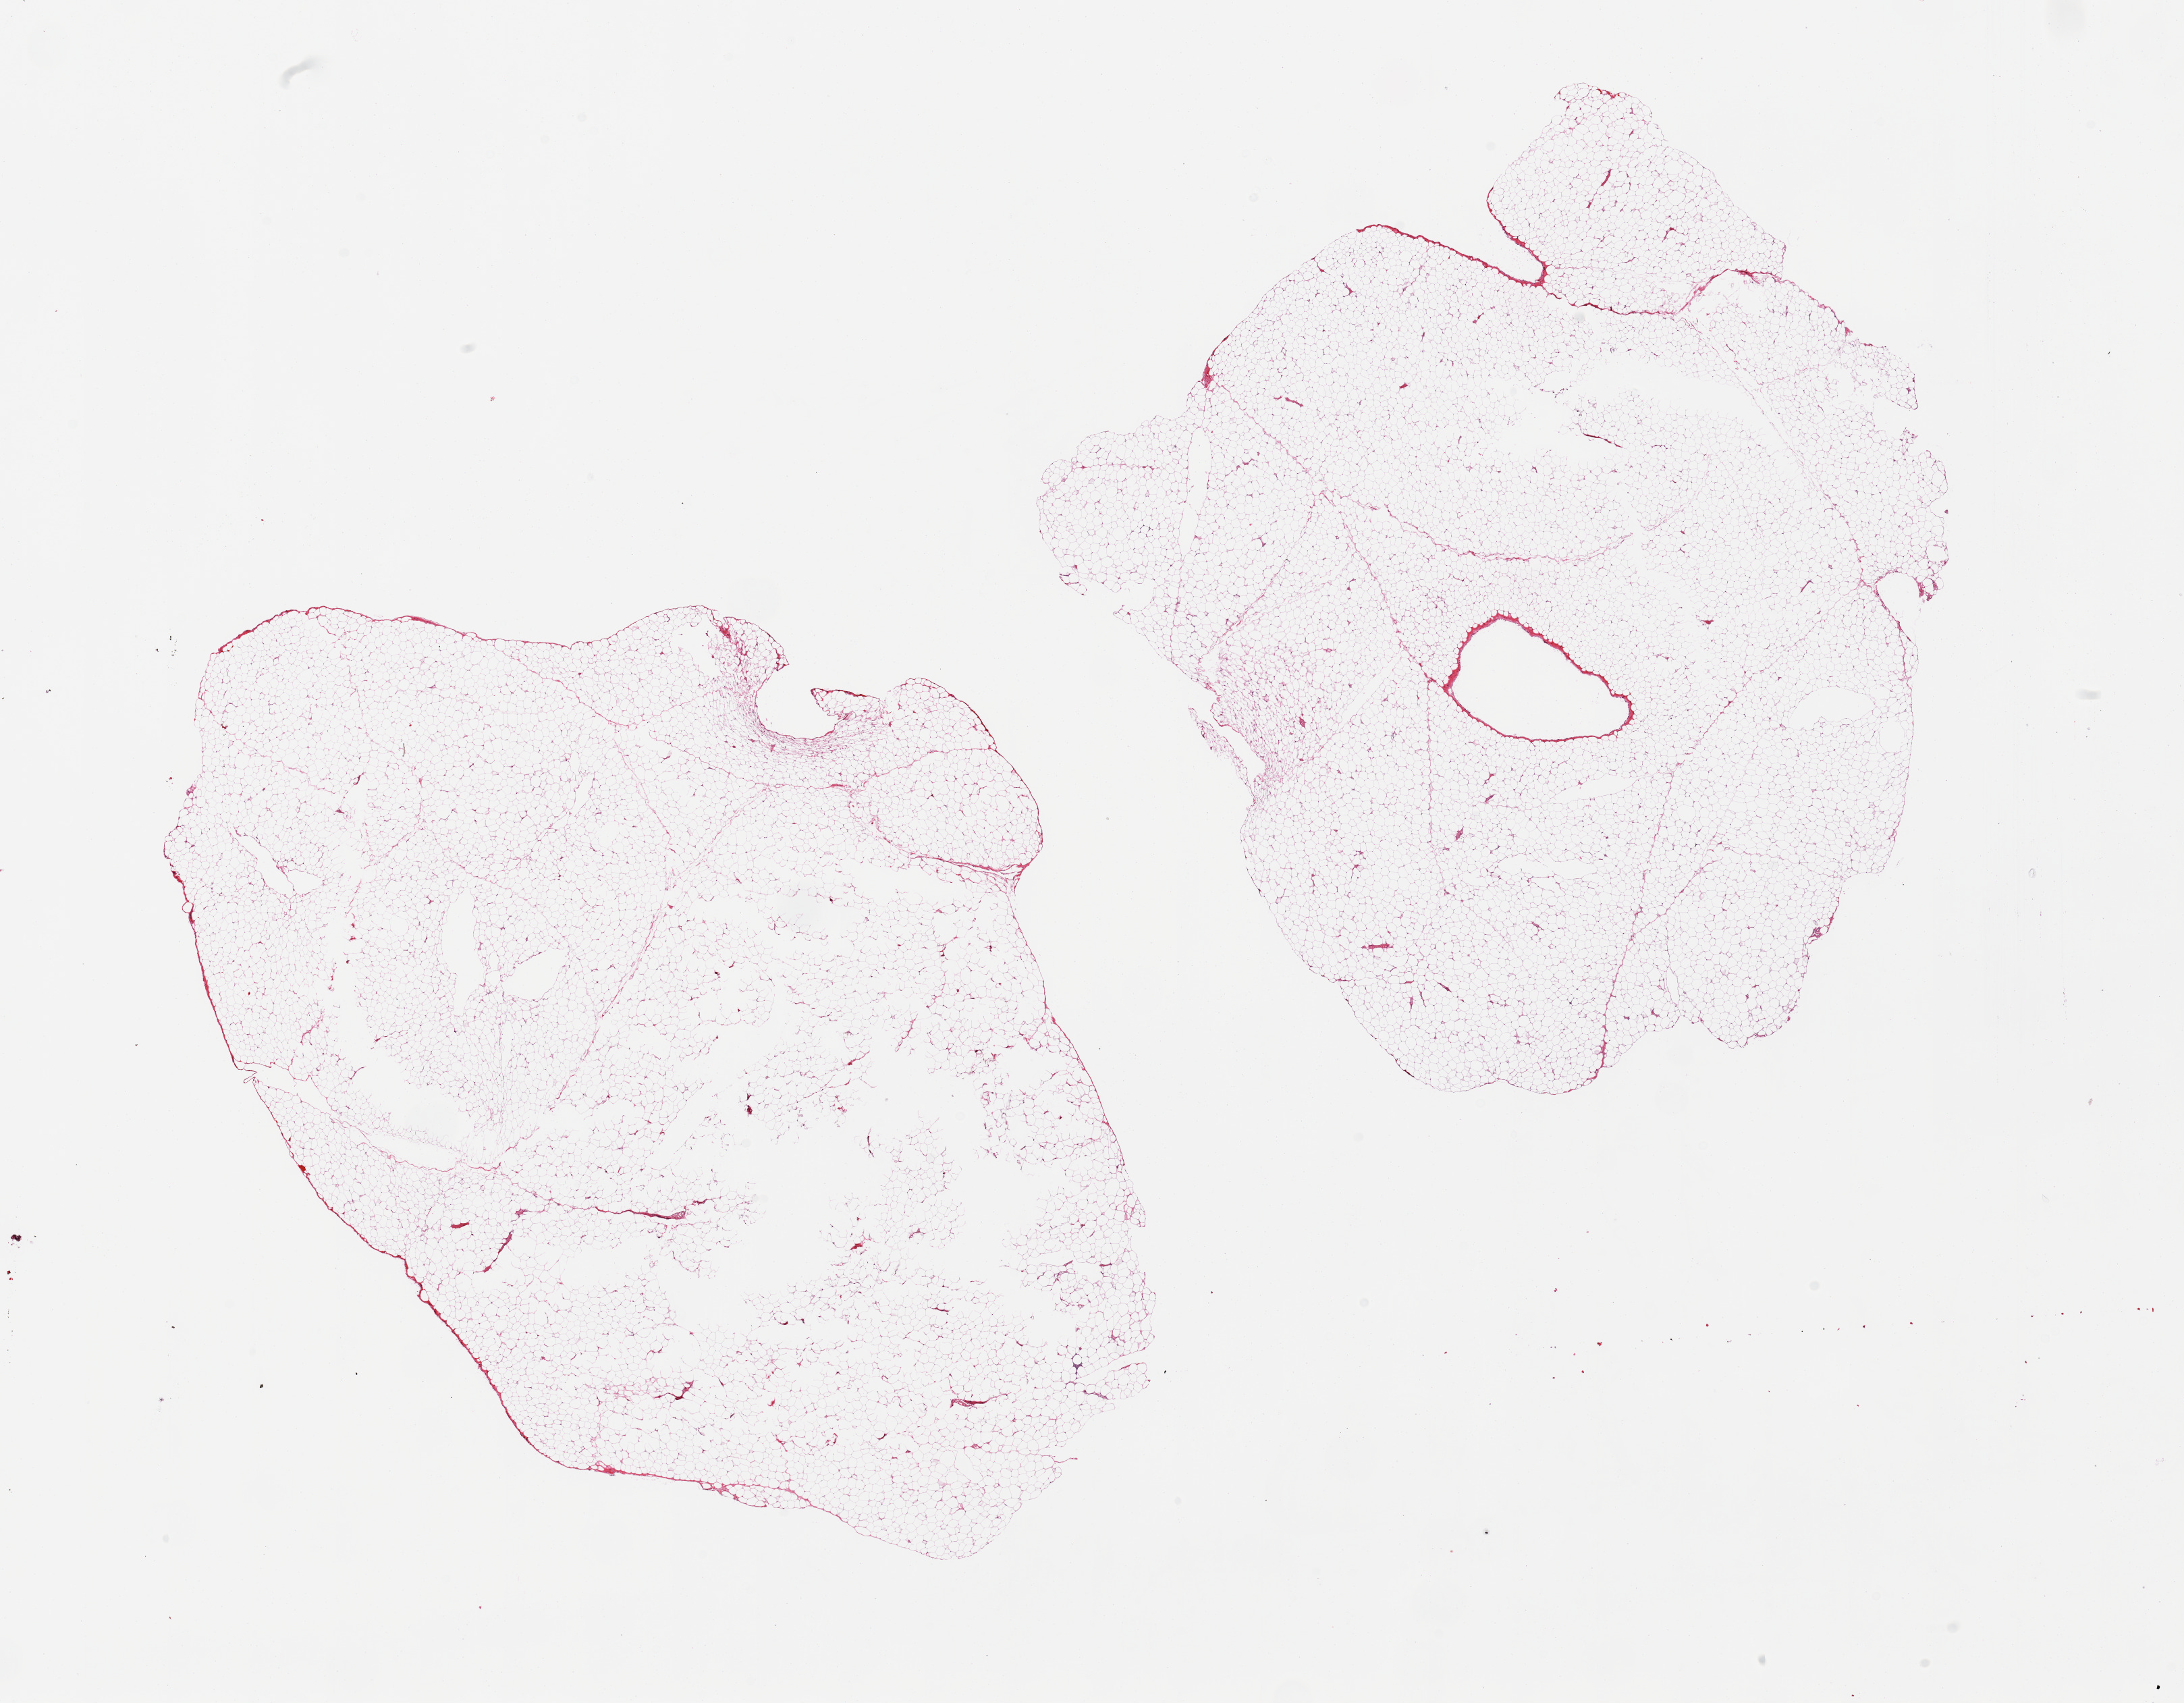
Digitized hematoxylin and eosin (H&E)-stained section, brightfield — low-resolution overview of the scanned area, about 25.6 x 20.0 mm; PAXgene-fixed paraffin-embedded (PFPE) section; sampled site (target tissue): omentum; donor tissue sample. Donor sex: male.
Pathologist's review note for this sample: 2 pieces.